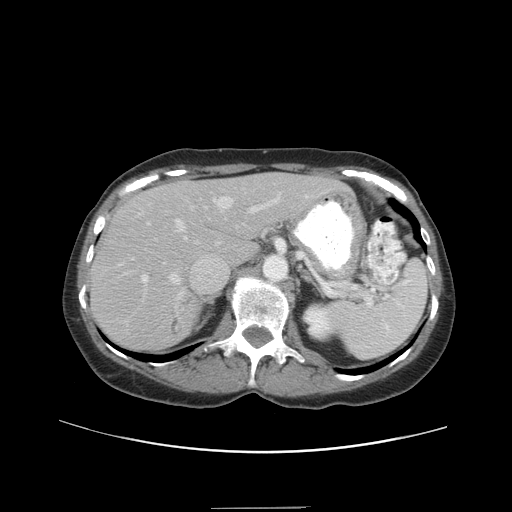
Contrast-enhanced abdominal CT, one axial slice. Slice 26 of 38 in the series (ordered by position). Reconstruction kernel STANDARD. 120 kVp. Intravenous contrast given. Soft-tissue window (W 400 / L 40 HU). 512 × 512 image matrix. Female patient, age 64 years. Case-level facts recorded for this patient, not image findings: diagnosis: colorectal cancer liver metastases, imaged before liver resection; multiple liver metastases: no; largest metastasis: 3.8 cm.
Structures marked on this image (expert manual segmentation):
- hepatic veins: bounding box [x1, y1, x2, y2] px = [168, 197, 232, 300]
- liver: [93, 174, 340, 350]
- planned liver remnant (the part of the liver to remain after resection): [137, 174, 340, 265]
- portal vein (with intrahepatic branches): [142, 193, 280, 282]